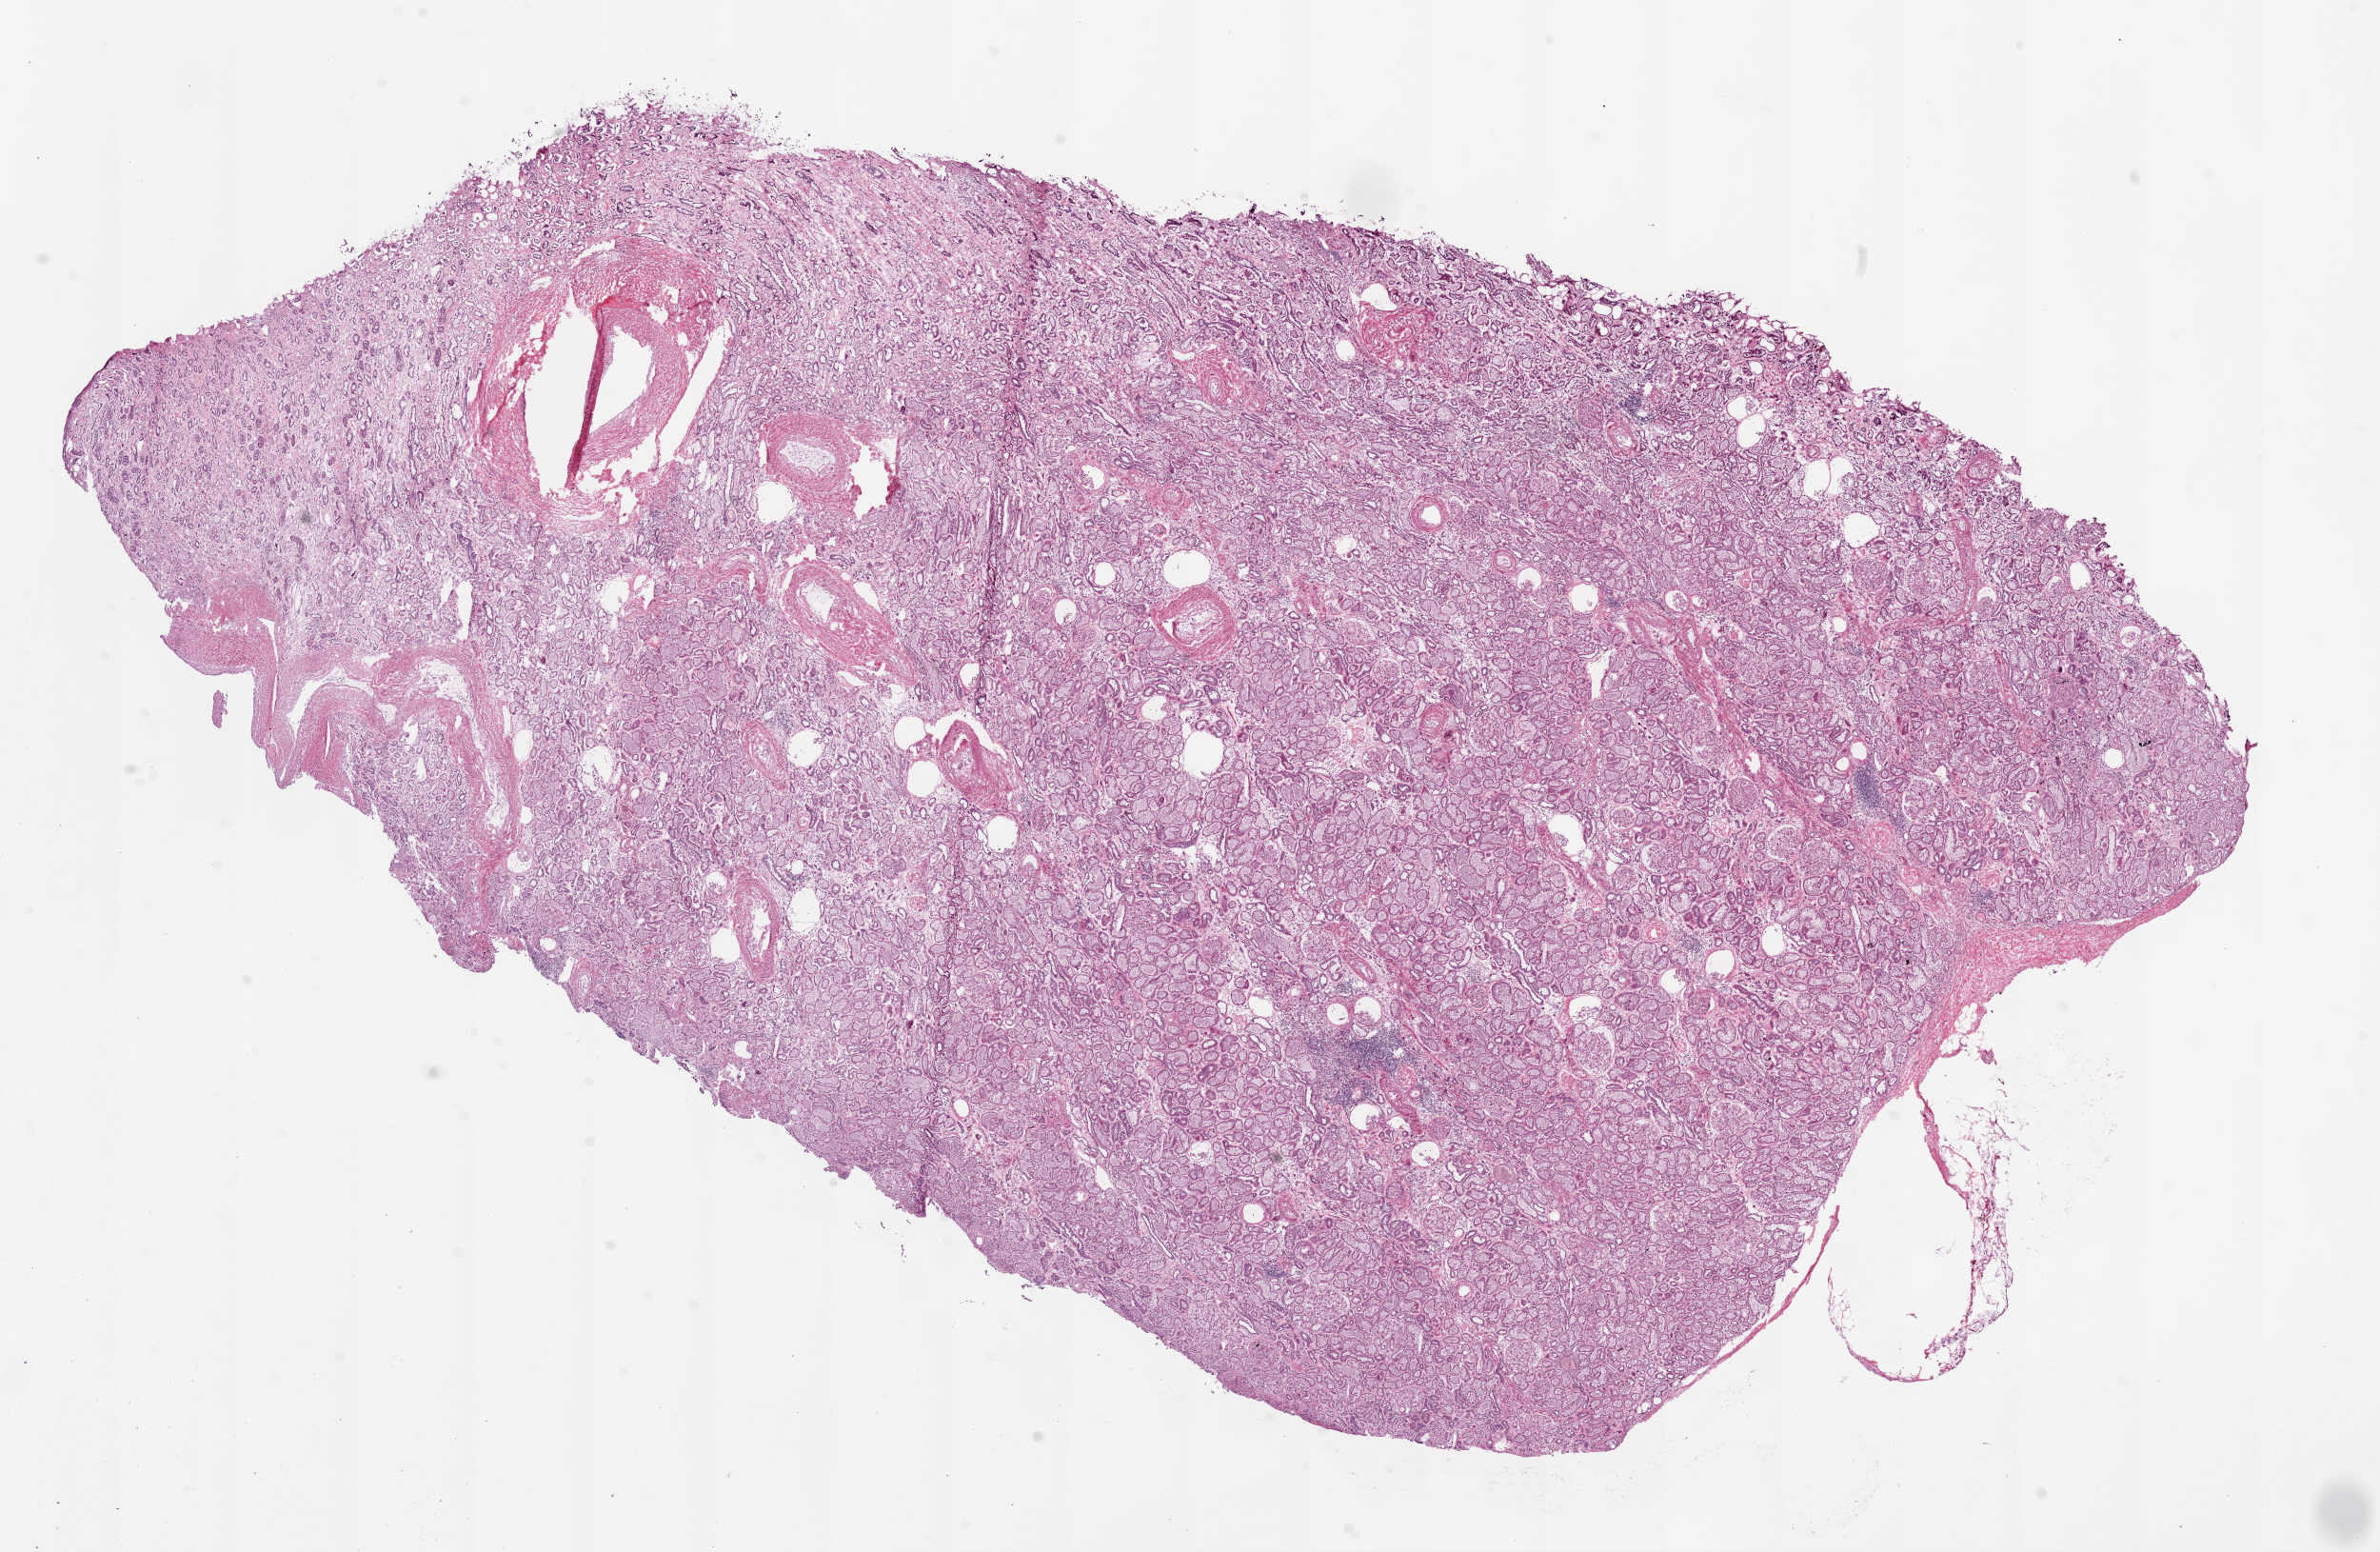
H&E-stained whole-slide image, shown as a low-resolution overview of the whole scanned area (about 20.1 x 13.1 mm). Frozen section. Sample: solid tissue normal (non-tumour tissue), kidney. Male, age 49 years at initial diagnosis.
• this section: solid tissue normal (non-tumour) sample from the same patient
• patient diagnosis: Clear cell adenocarcinoma, NOS